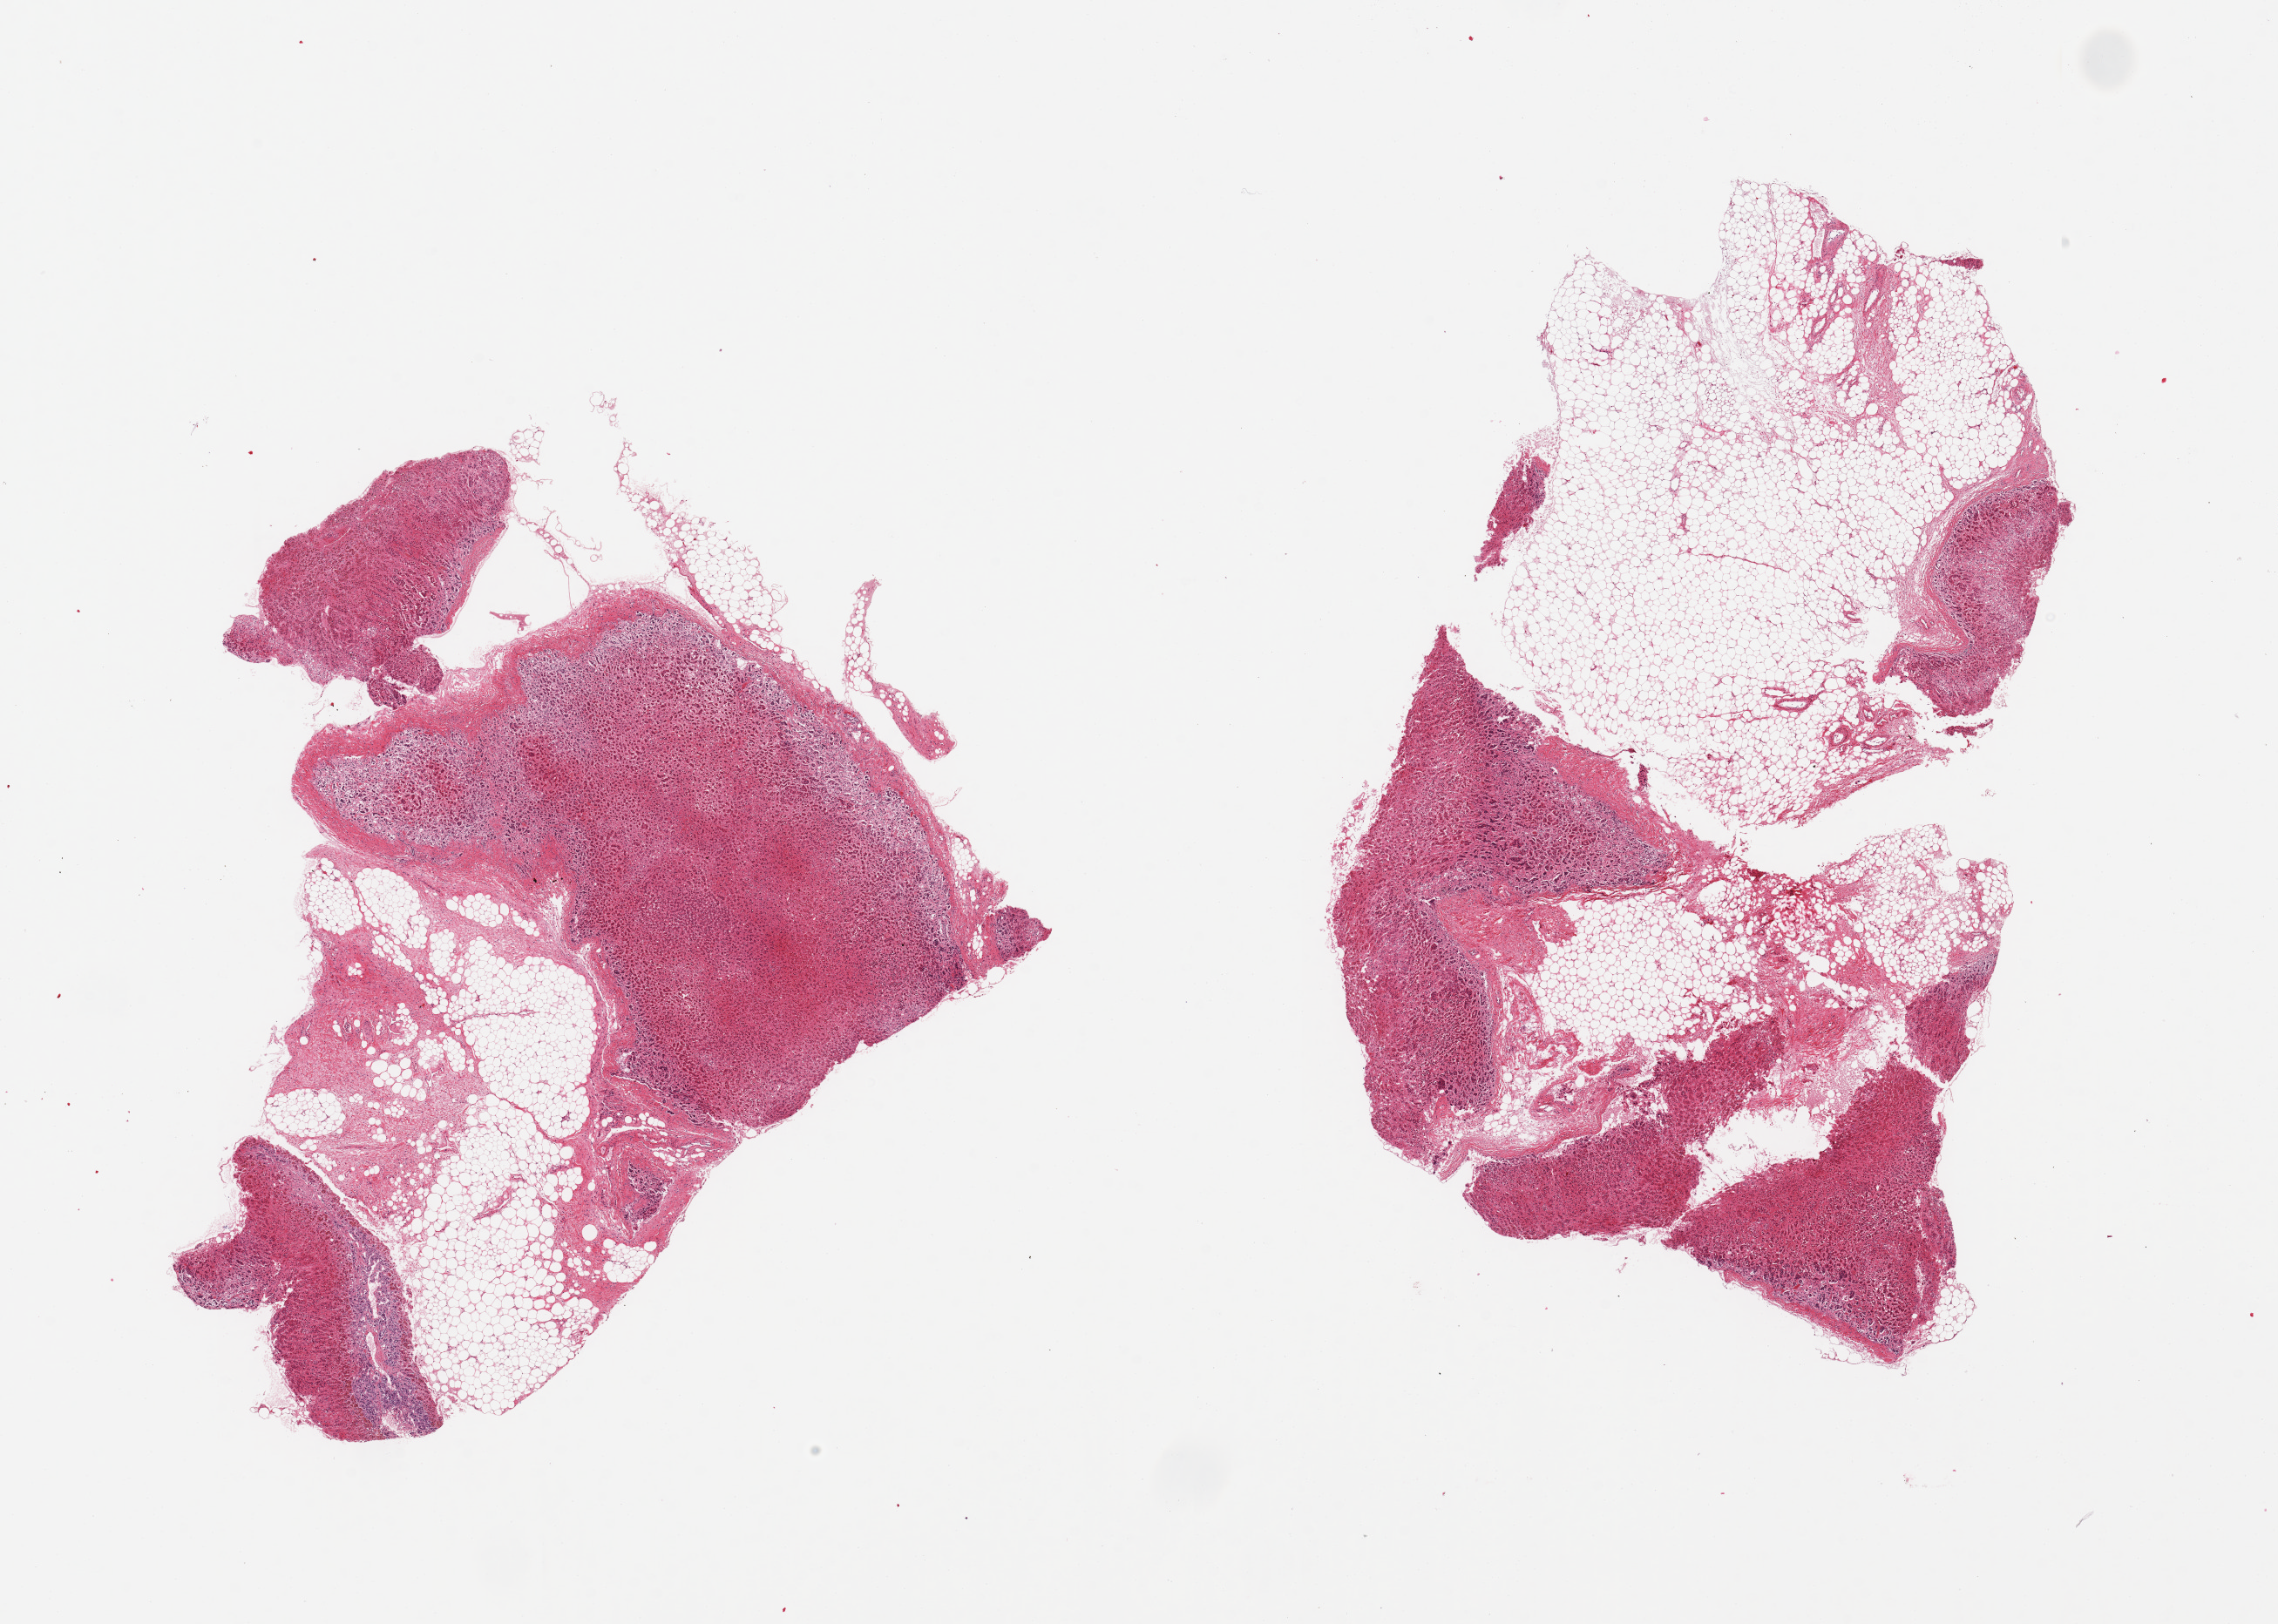
Digitized haematoxylin and eosin-stained section, brightfield — low-resolution overview of the scanned area, about 20.7 x 14.7 mm; PAXgene-fixed paraffin-embedded (PFPE) section; target tissue: adrenal gland; donor tissue sample.
* review note (as recorded): 2 pieces; moderately autolyzed adrenal cortex and medulla, ~40% and 50% internal/external fat